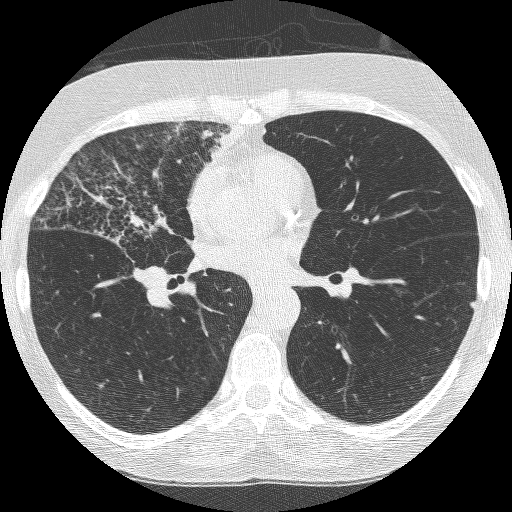
Low-dose screening chest CT, axial slice, third annual screen, lung window (W 1500 / L -600 HU), 1.25 mm slice thickness, slice 131 of 253 in the series, 512 × 512 image matrix, field of view 294 × 294 mm. Female participant, aged 64 years at enrolment.
Lesion marked by an expert reader, bounding box <55,160,200,308> (left, top, right, bottom; pixels). Screening reader's record for this exam (one nodule recorded; not confirmed to be the boxed lesion): non-calcified nodule or mass ≥4 mm, right upper lobe, 49 × 43 mm, spiculated (stellate) margins, soft tissue attenuation, pre-existing on the prior screen: yes; interval growth: yes. Official screen result: positive, other. Lung cancer was diagnosed 7 days after this screen: adenocarcinoma, NOS, right upper lobe, right middle lobe, right hilum, stage IV (AJCC 6th edition), 85 mm at pathology.